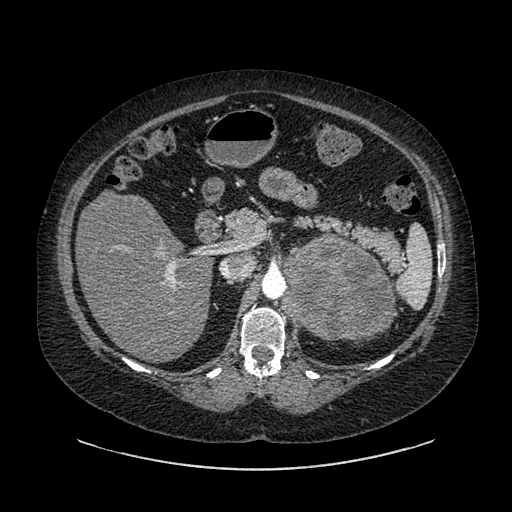
Contrast-enhanced abdominal CT, one axial slice. Slice 568 of 769 in the series (ordered by position). 120 kVp. Intravenous contrast given. Soft-tissue window (W 400 / L 40 HU). 0.62 mm slice thickness. 512 × 512 image matrix. Patient: female, 61 years. Case-level facts recorded for this patient, not image findings: diagnosis: adrenocortical carcinoma; tumour side: left adrenal; tumour size at pathology: 13 cm; Ki-67 index: 79 %; stage (as recorded): 2.
Outlined on this slice (semi-automatically segmented with operator editing):
- mass: bounding box <281,234,391,338> (left, top, right, bottom; pixels)